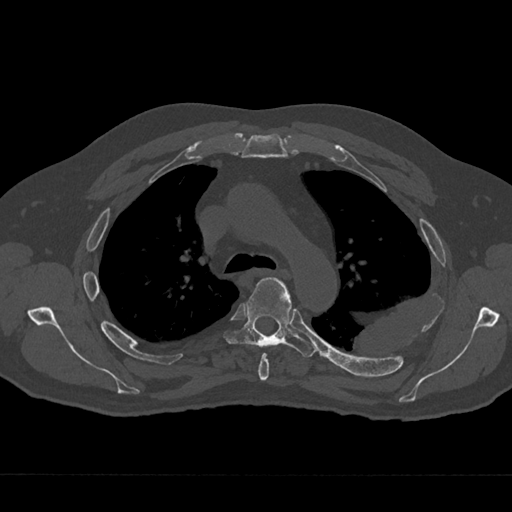
CT including the spine, one axial slice; position 486 of 797 along the scan axis; reconstruction kernel Br40s/3; bone window (W 1800 / L 400 HU); 0.5 mm slice thickness; 512 × 512 image matrix, field of view 377 × 377 mm. Patient: male, 75 years. Case-level facts recorded for this patient, not image findings: primary cancer: renal; vertebrae with lytic lesions (as recorded): T4.
Annotated regions visible in this slice (semi-automatically segmented with operator editing):
- T4 vertebra: bounding box <258,353,269,381> (left, top, right, bottom; pixels)
- T5 vertebra: <224,278,317,358>